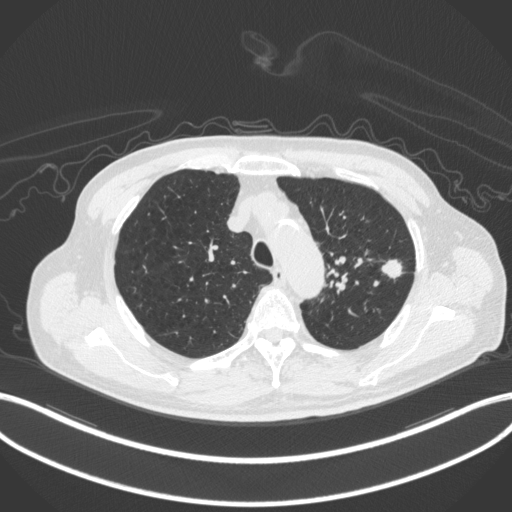
Chest CT, one axial slice; position 341 of 420 along the scan axis; reconstruction kernel B31f; 120 kVp; lung window (W 1500 / L -600 HU); 512 × 512 image matrix, field of view 400 × 400 mm. Male patient, age 77 years. From the clinical record (not read from this slice): clinical TNM (as recorded): T3 N1 M0.
Structures marked on this image (rectangle marked by the reading radiologist):
- lung tumour (recorded histology: adenocarcinoma): box from (x=379, y=254) to (x=408, y=281) px